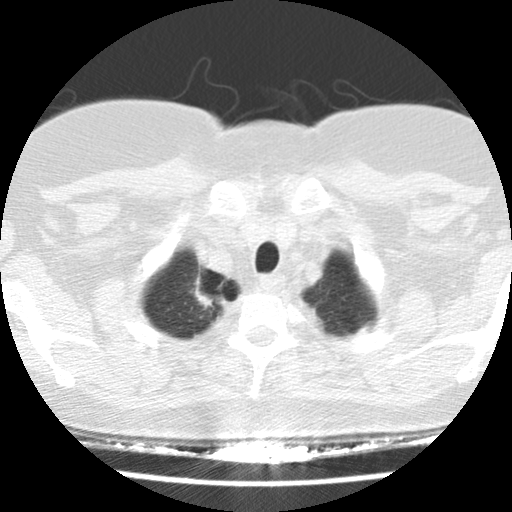
Low-dose screening chest CT, one axial slice; reconstruction kernel STANDARD; 120 kVp; lung window (W 1500 / L -600 HU); 512 × 512 image matrix.
Outlined on this slice (expert manual segmentation):
- lesion 1 (tumor, upper lobe of right lung): bounding box <194,279,226,308> (left, top, right, bottom; pixels)